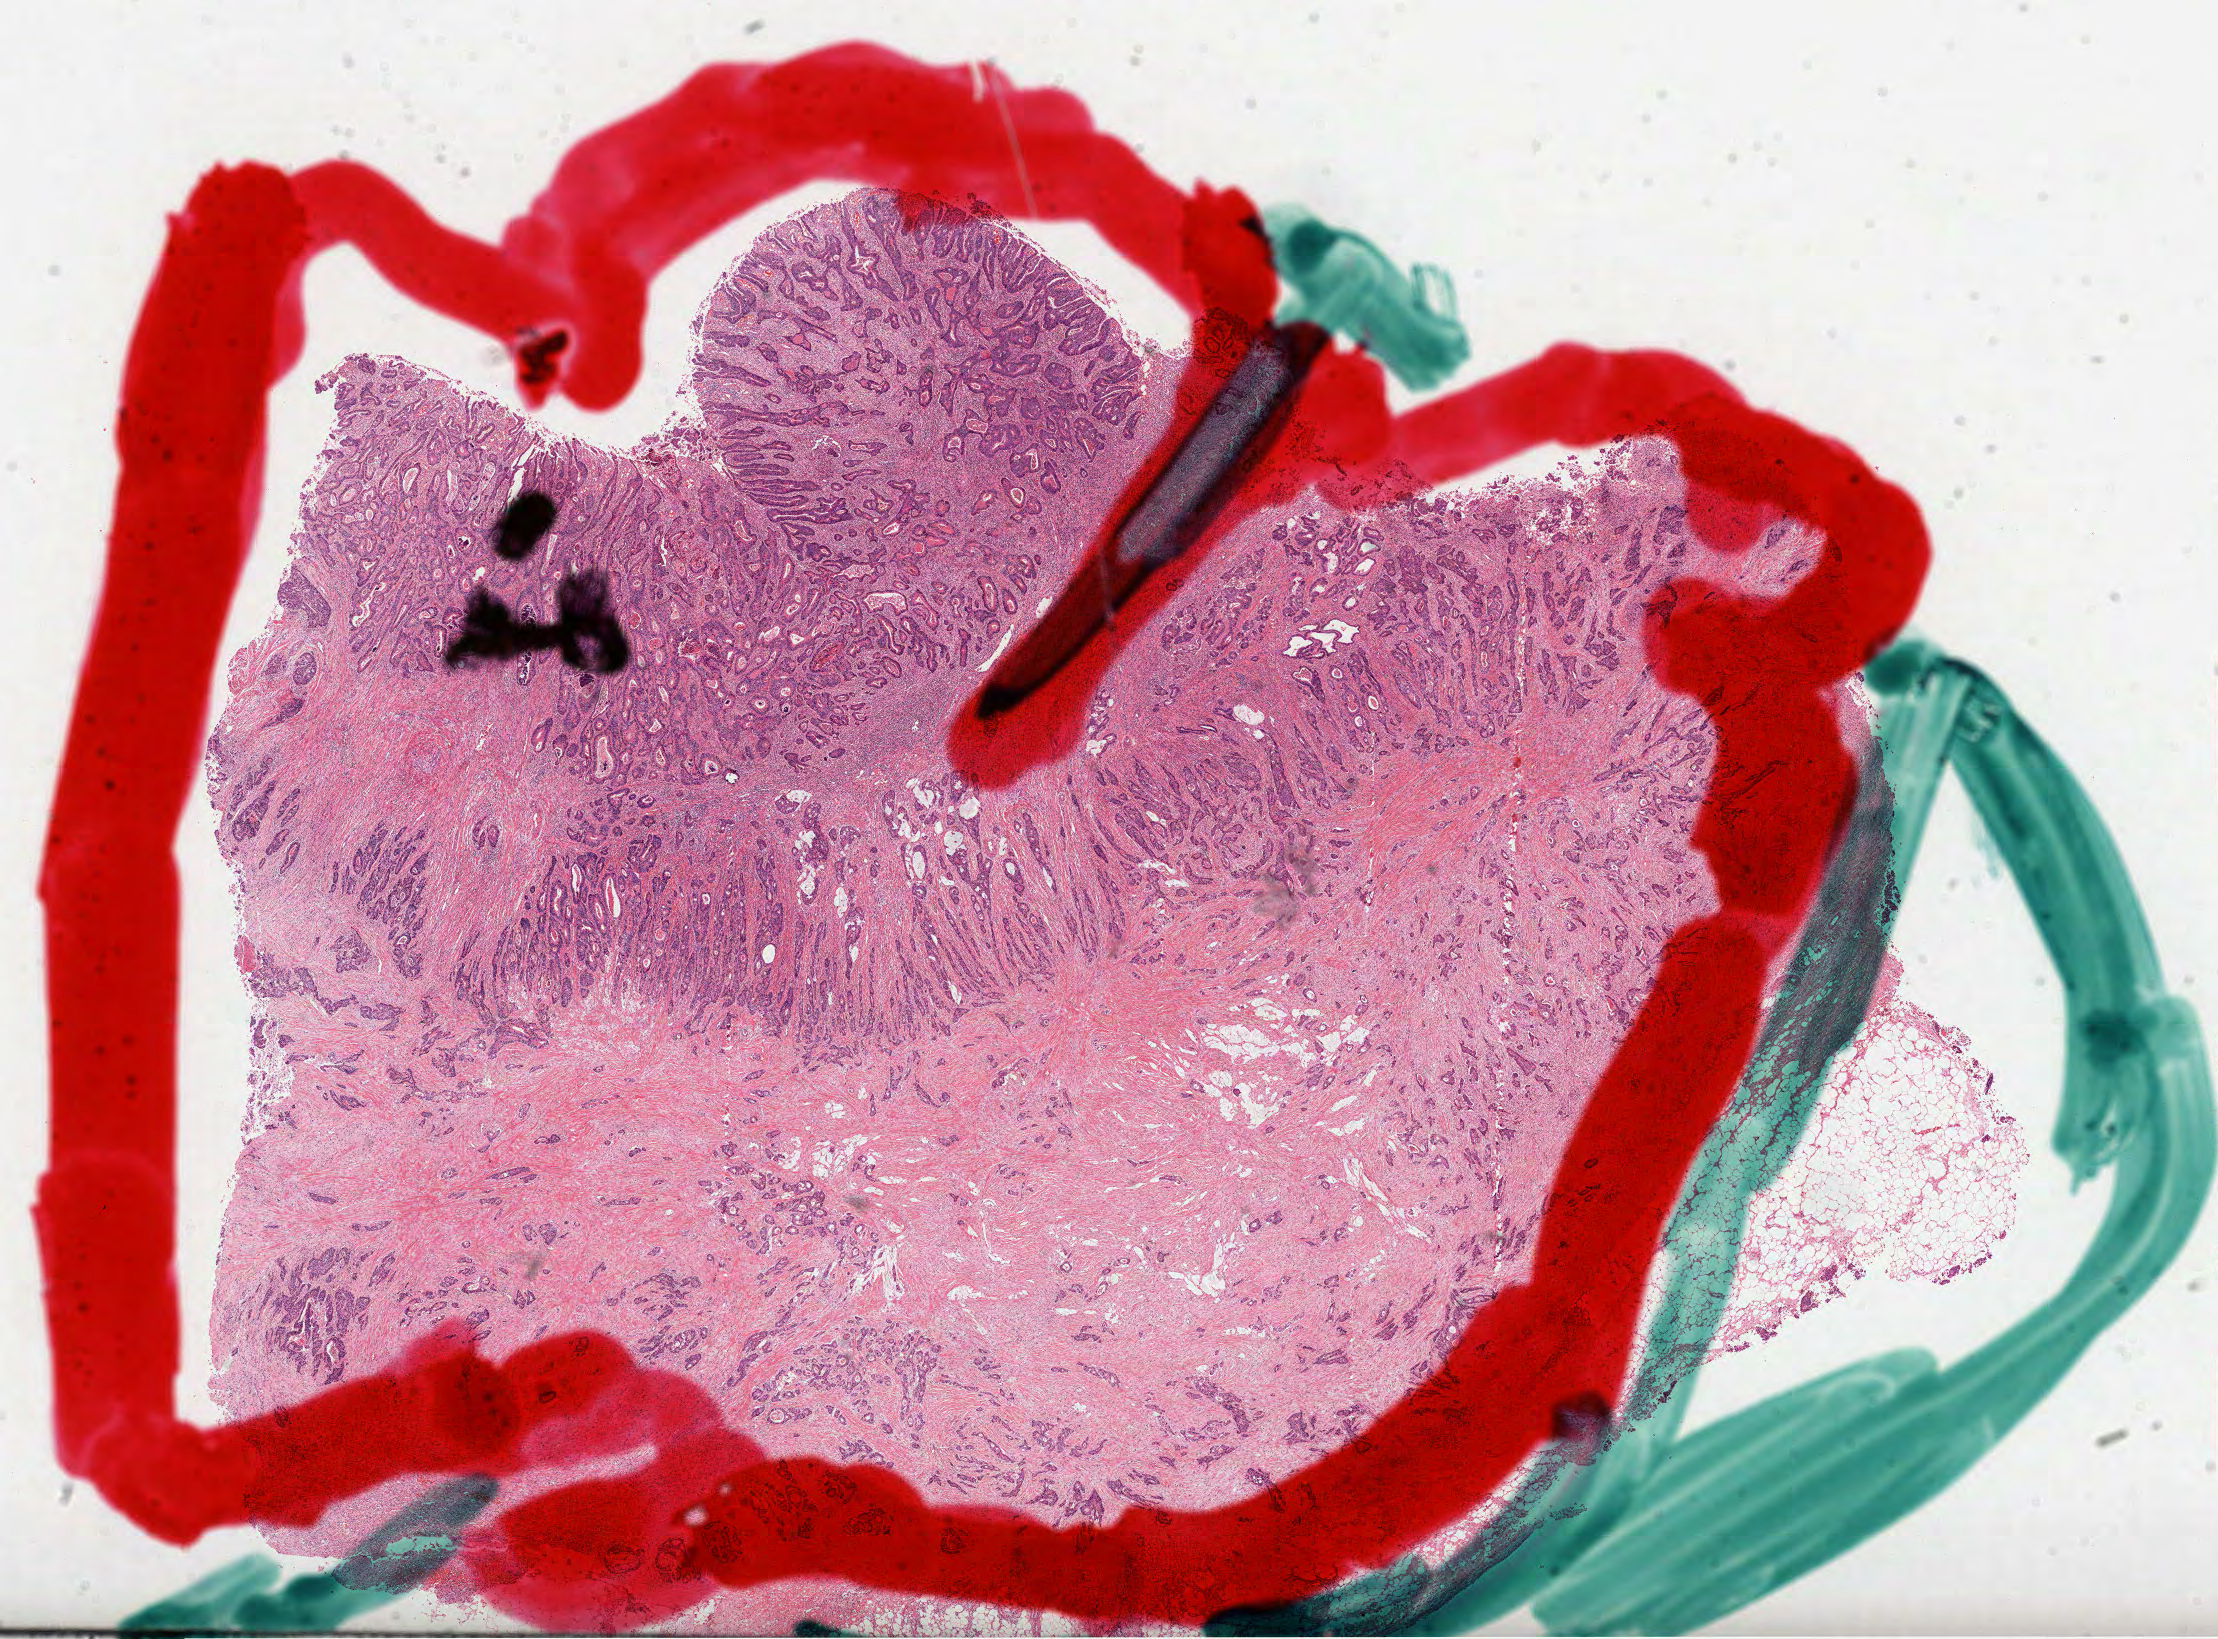
Hematoxylin and eosin (H&E) stained whole-slide image — whole scanned area (about 17.9 x 13.2 mm, acquisition: 40x scan) shown as a low-resolution overview; formalin-fixed paraffin-embedded (FFPE) diagnostic section; primary tumour sample from the rectum. Patient: female, age at initial diagnosis 74 years.
Diagnosis: Adenocarcinoma, NOS.